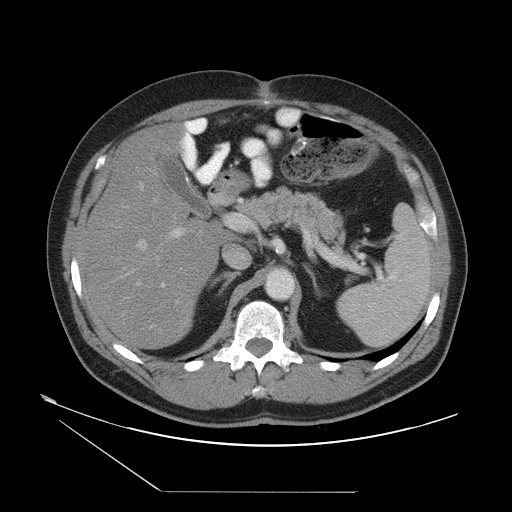
Contrast-enhanced abdominal CT, one axial slice. Position 28 of 55 along the scan axis. Intravenous contrast given. Soft-tissue window (W 400 / L 40 HU). 5 mm slice thickness. 512 × 512 image matrix, field of view 454 × 454 mm. Male patient, age 59 years. Case-level facts recorded for this patient, not image findings: diagnosis: colorectal cancer liver metastases, imaged before liver resection; multiple liver metastases: yes; largest metastasis: 0.3 cm; disease in both lobes: yes.
Structures marked on this image (manually delineated by an expert):
- hepatic veins: bounding box (x1, y1, x2, y2) in pixels: (121, 227, 175, 328)
- liver: (86, 129, 222, 348)
- planned liver remnant (the part of the liver to remain after resection): (86, 138, 222, 348)
- portal vein (with intrahepatic branches): (160, 216, 201, 304)